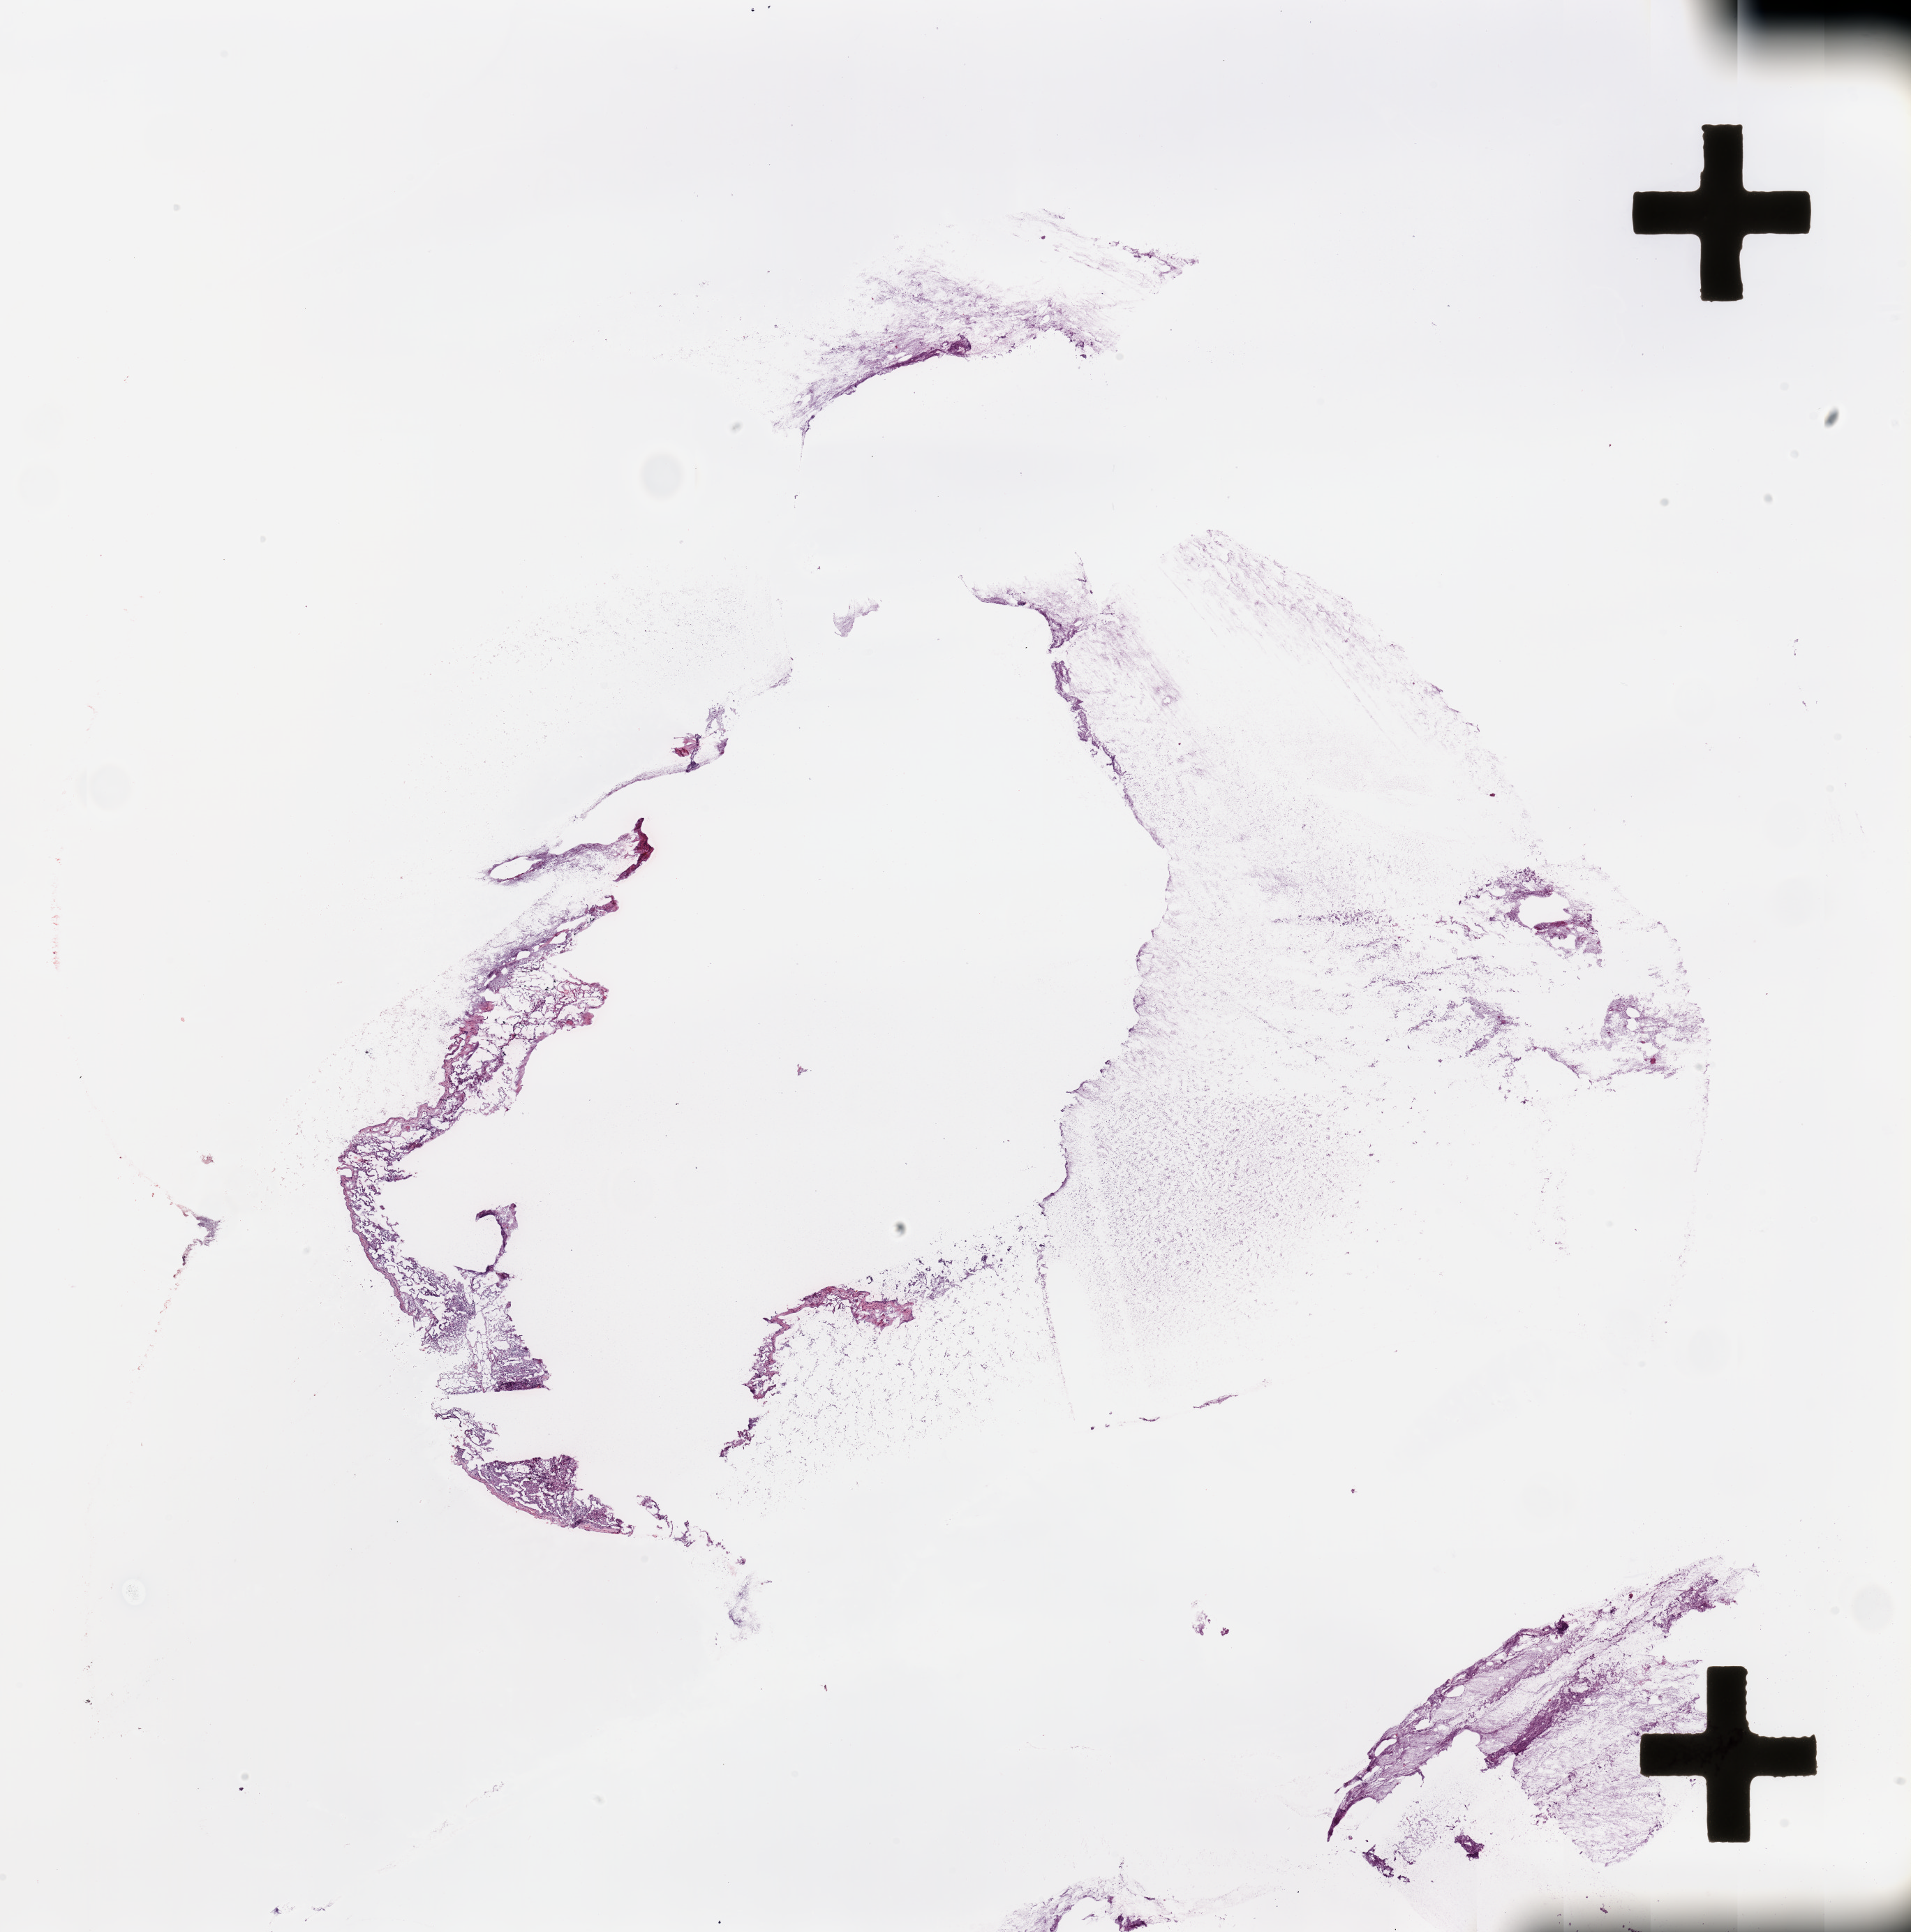
Digitized H&E tissue section (whole slide), a low-resolution overview of the entire scanned area, about 21.7 x 21.9 mm (from a 20x scan). Normal (non-tumour) tissue sample, lung. Male, 79 y/o.
This section: normal (non-tumour) tissue from the same patient. Patient diagnosis: Adenocarcinoma, NOS.